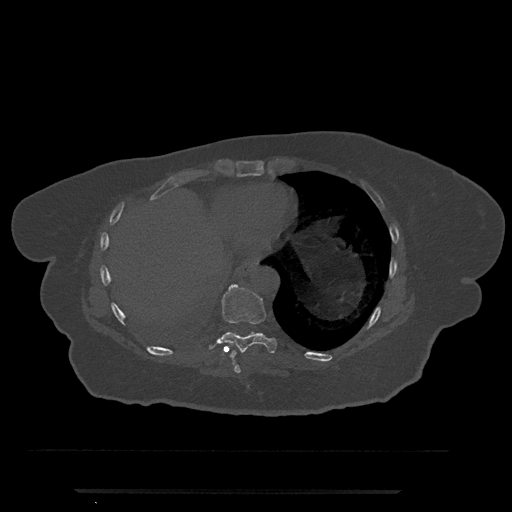
CT including the spine, one axial slice; position 335 of 797 along the scan axis; reconstruction kernel Br40s/3; bone window (W 1800 / L 400 HU); 0.5 mm slice thickness; 512 × 512 image matrix. Female patient, age 51 years. Case-level facts recorded for this patient, not image findings: primary cancer: neuro; vertebrae with lytic lesions (as recorded): T8.
Annotated regions visible in this slice (semi-automatic segmentation, software-assisted and operator-edited):
- T8 vertebra: bounding box (x1, y1, x2, y2) in pixels: (234, 365, 241, 373)
- T9 vertebra: (208, 284, 277, 358)